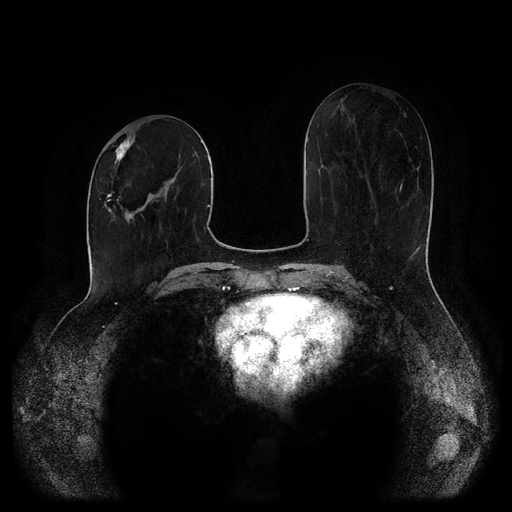
Breast MRI (dynamic contrast-enhanced, multi-phase), one axial slice; position 41 of 116 along the scan axis; dynamic contrast-enhanced series, time point 2 of 5 at this slice position (early post-contrast); 1.5 T; TE 2.6 ms, TR 5.2 ms; 2 mm slice thickness; 512 × 512 image matrix. Patient: female, 52 years.
Outlined on this slice (semi-automatic segmentation, software-assisted and operator-edited):
- breast lesion (labelled 'tumour' in the annotation; benign lesions carry a separate 'benign' label): box from (x=112, y=135) to (x=134, y=164) px